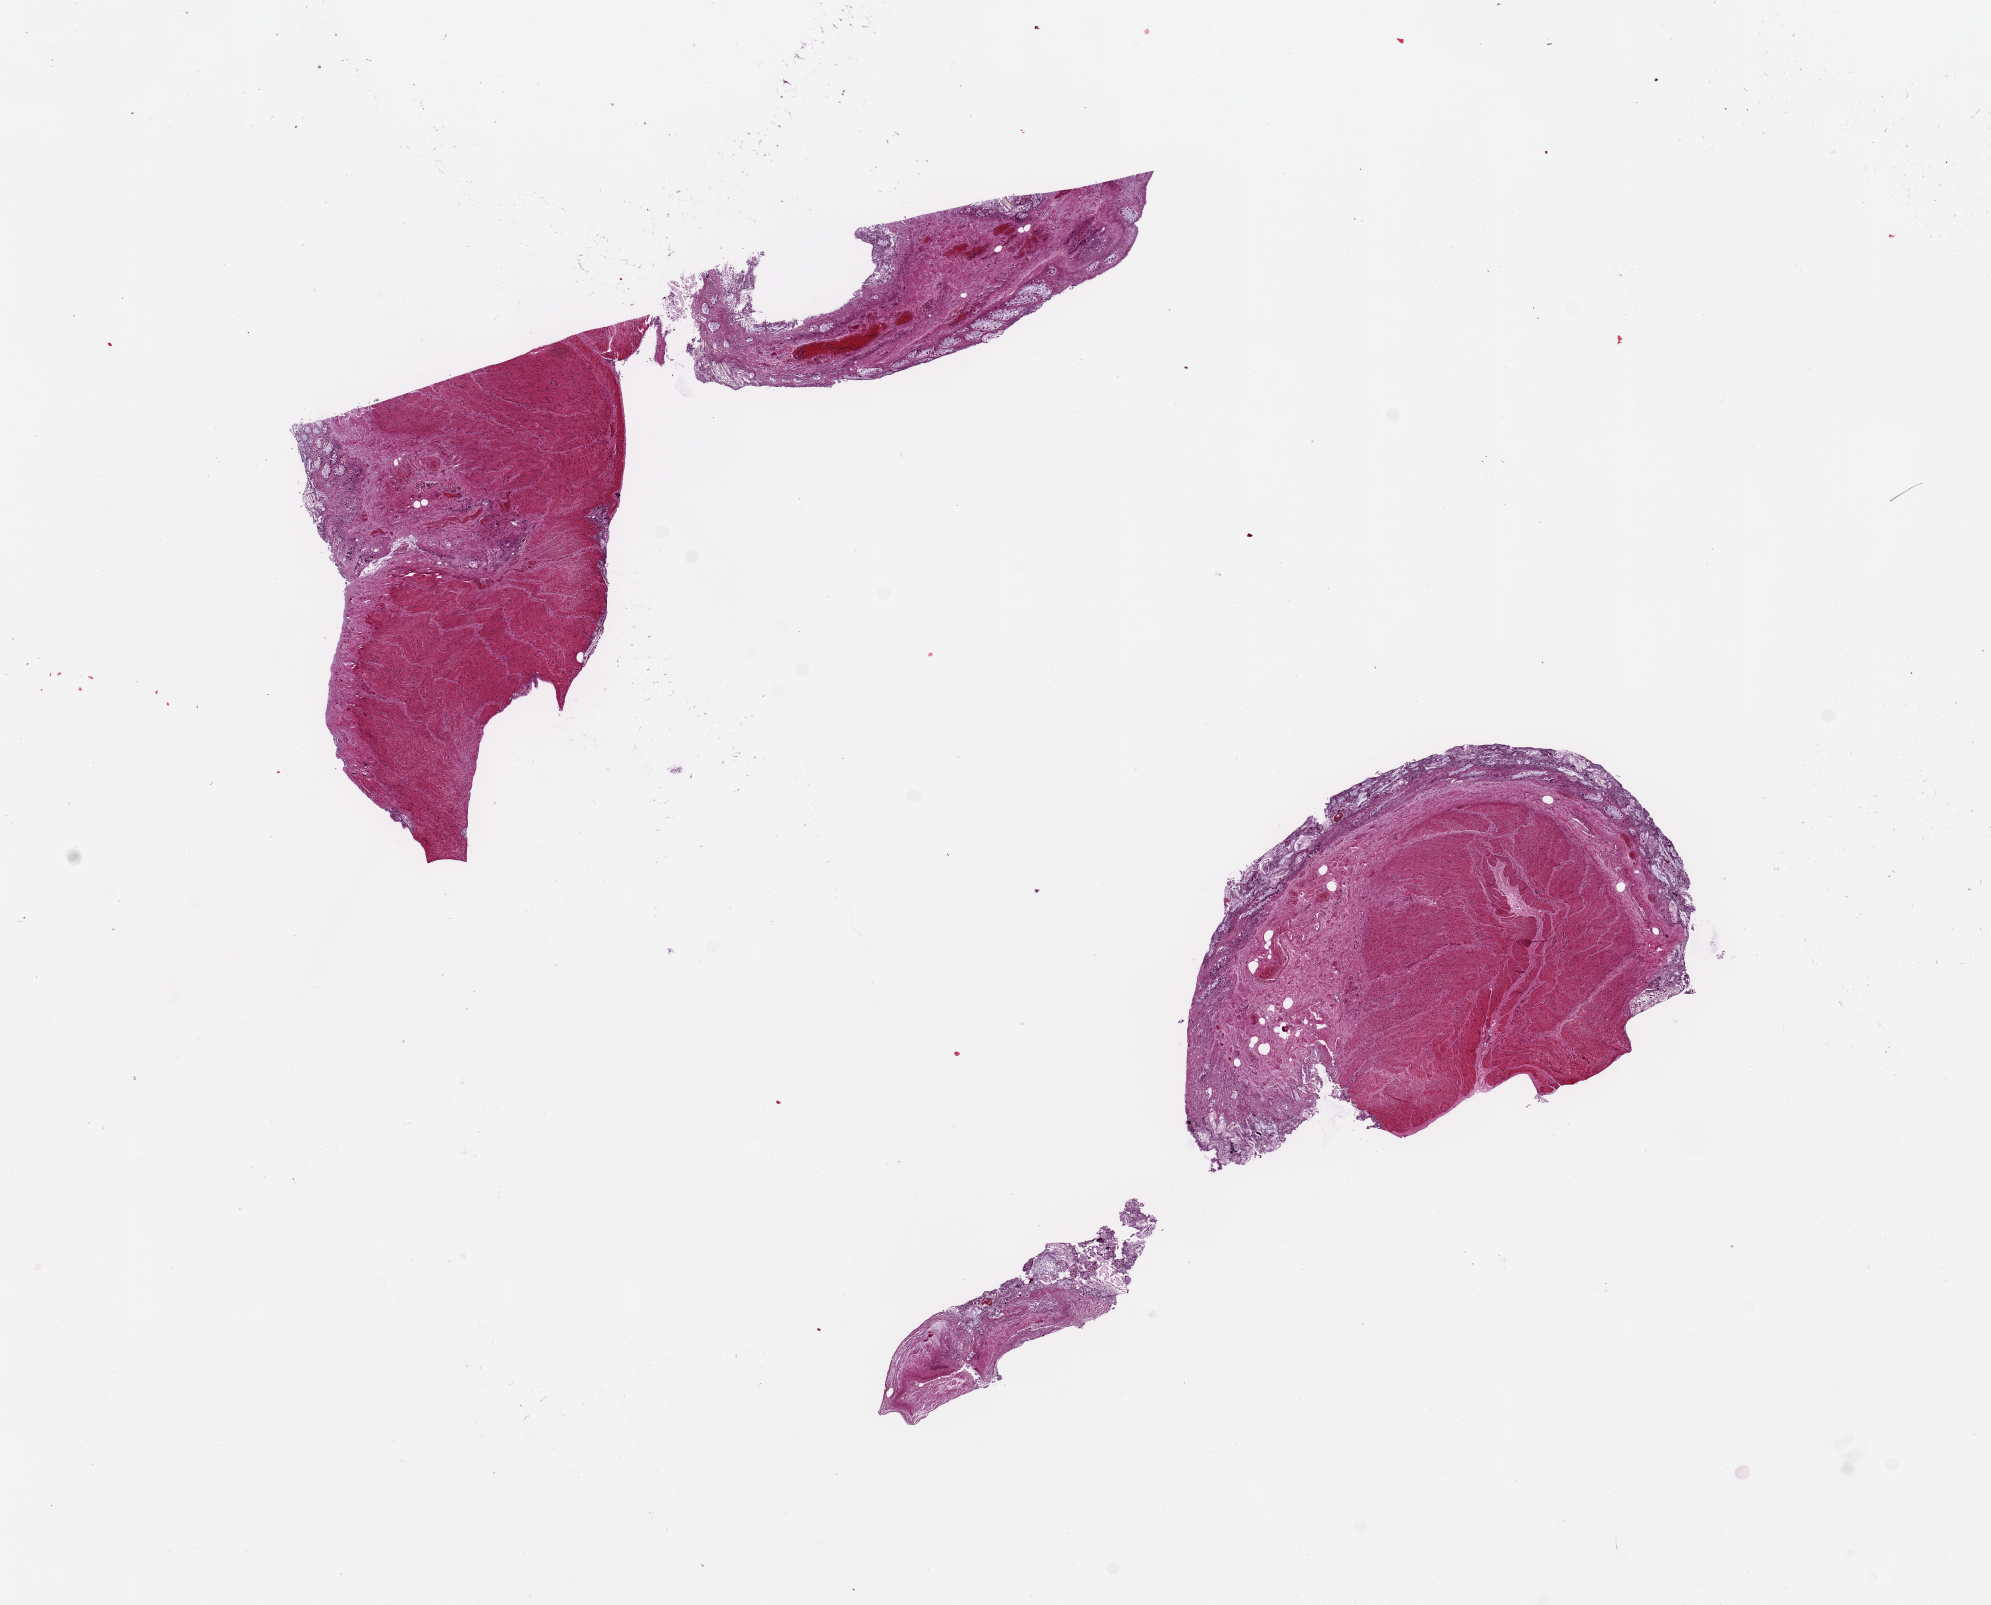
Digitized H&E-stained section — whole scanned area (about 15.8 x 12.7 mm, acquisition: 20x scan) shown as a low-resolution overview. PAXgene-fixed, paraffin-embedded tissue. Section of transverse colon (target tissue). Donor tissue sample. Female donor.
Review note (as recorded): Mucosa completely autolytic; only viable tissue is muscularis propria and adipose.